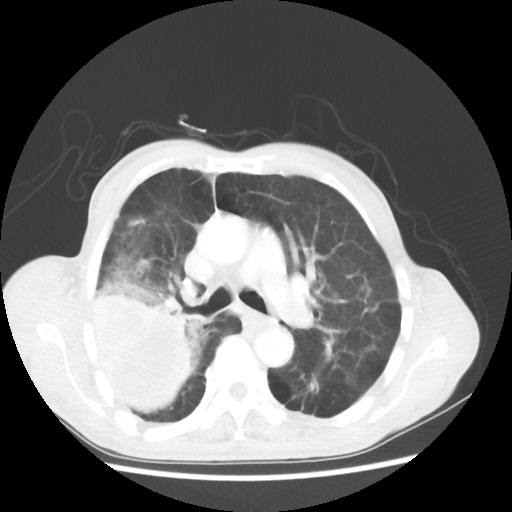
Chest CT, one axial slice. Position 35 of 58 along the scan axis. 100 kVp. Lung window (W 1500 / L -600 HU). 5 mm slice thickness. 512 × 512 image matrix, field of view 351 × 351 mm. Male patient, age 75 years. From the clinical record (not read from this slice): clinical TNM (as recorded): T4 N1 M1.
Annotated regions visible in this slice (bounding box drawn by a radiologist):
- lung tumour (recorded histology: adenocarcinoma): bounding box <84,268,205,413> (left, top, right, bottom; pixels)